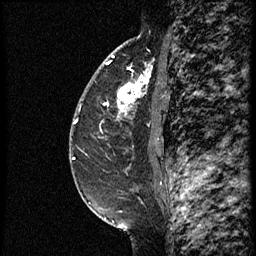
Breast MRI (dynamic contrast-enhanced), one sagittal slice. Position 41 of 60 along the scan axis. Dynamic contrast-enhanced study with each time point stored as its own series, time point 2 of 3 at this slice position (early post-contrast, ordered by acquisition time). 1.5 T. TE 4.2 ms, TR 18.9 ms. 2 mm slice thickness. 256 × 256 image matrix, field of view 200 × 200 mm. Female patient. Case-level facts recorded for this patient, not image findings: setting: breast cancer imaged before/during neoadjuvant chemotherapy; receptor status: HER2-positive.
Structures marked on this image (semi-automatic segmentation, software-assisted and operator-edited):
- analysis volume of interest (the breast-tissue region the enhancement analysis was run in; not a lesion): bounding box [x1, y1, x2, y2] px = [77, 64, 161, 147]
- tumour enhancement mask (voxels above the 100 % enhancement threshold inside the analysis volume of interest): [118, 65, 151, 118]